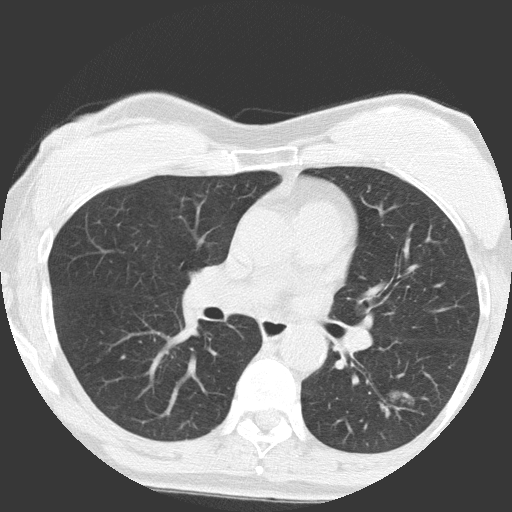
Low-dose screening chest CT, axial slice; baseline annual screen; lung window (W 1500 / L -600 HU); lung (sharp) reconstruction kernel (FC51); slice 66 of 149 in the series. Female, age 64 years at enrolment.
- Lesion marked by an expert reader, bounding box <357,373,440,449> (left, top, right, bottom; pixels).
- The exam's reader record, not a measurement of the box and not confirmed to be the same lesion: non-calcified nodule or mass ≥4 mm, right upper lobe, 4 × 4 mm, poorly defined margins, ground glass attenuation.
- Note: the box lies in the patient's left hemithorax on this image, whereas the reader's record names the right lung; they may be different findings.
- Official screen result: positive, change unspecified: nodule(s) >= 4 mm or enlarging nodule(s), mass(es), or other non-specific abnormalities suspicious for lung cancer.
- Participant outcome: lung cancer diagnosed 932 days after this screen — adenocarcinoma, NOS, left lower lobe, moderately differentiated (G2), stage IA (AJCC 6th edition), 17 mm at pathology.